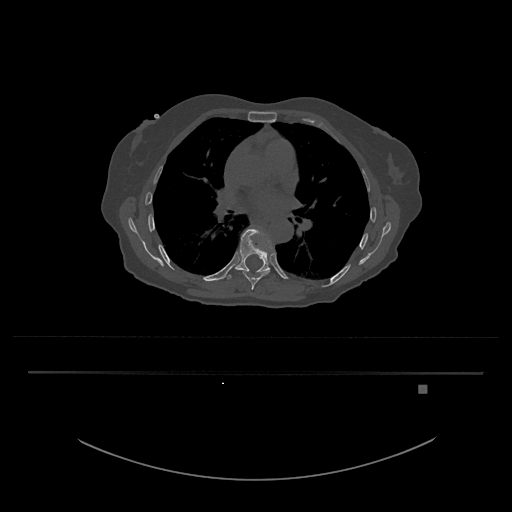
CT including the spine, one axial slice. 120 kVp. Bone window (W 1800 / L 400 HU). 0.5 mm slice thickness. 512 × 512 image matrix. Female patient, age 57 years. From the clinical record (not read from this slice): primary cancer: cervical.
Outlined on this slice (semi-automatically segmented with operator editing):
- T8 vertebra: bounding box <242,270,268,290> (left, top, right, bottom; pixels)
- T9 vertebra: <225,227,274,280>